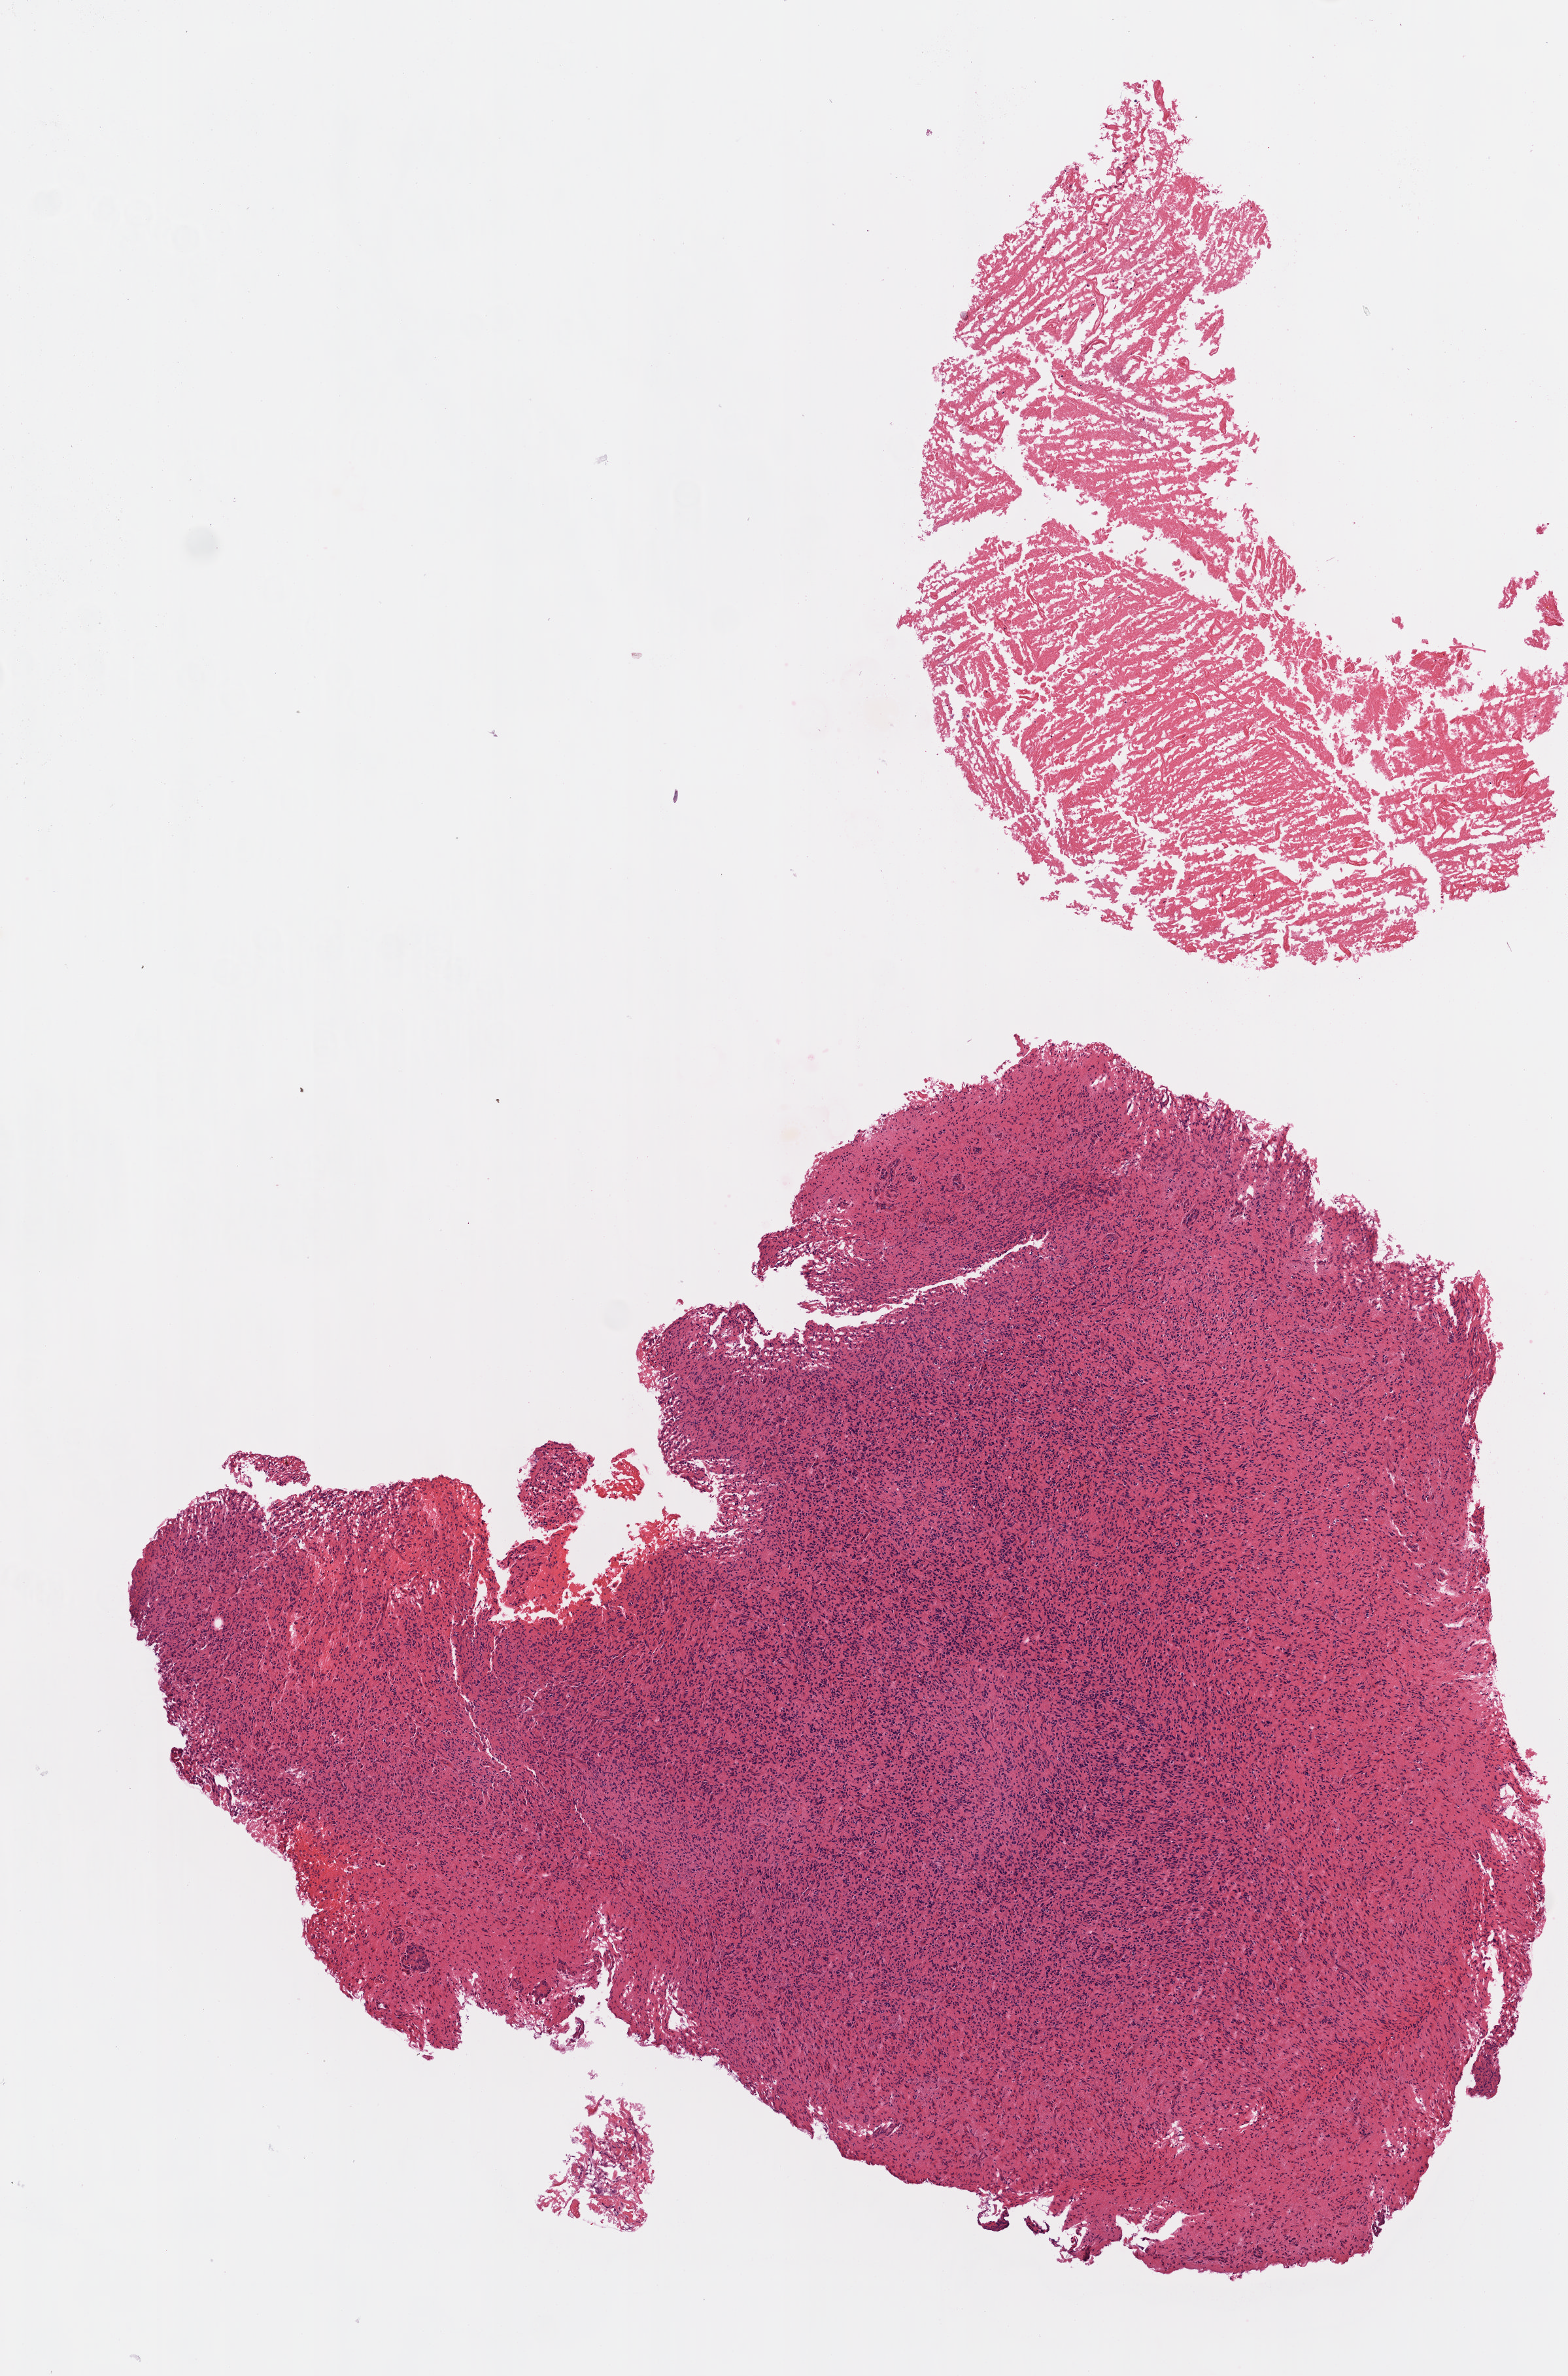
H&E whole-slide image, whole scanned area (about 4.8 x 7.3 mm, acquisition: 20x scan) shown as a low-resolution overview. FFPE section. Brain, primary tumour sample. Female patient; age at initial diagnosis 63 years.
- pathologic diagnosis: Glioblastoma